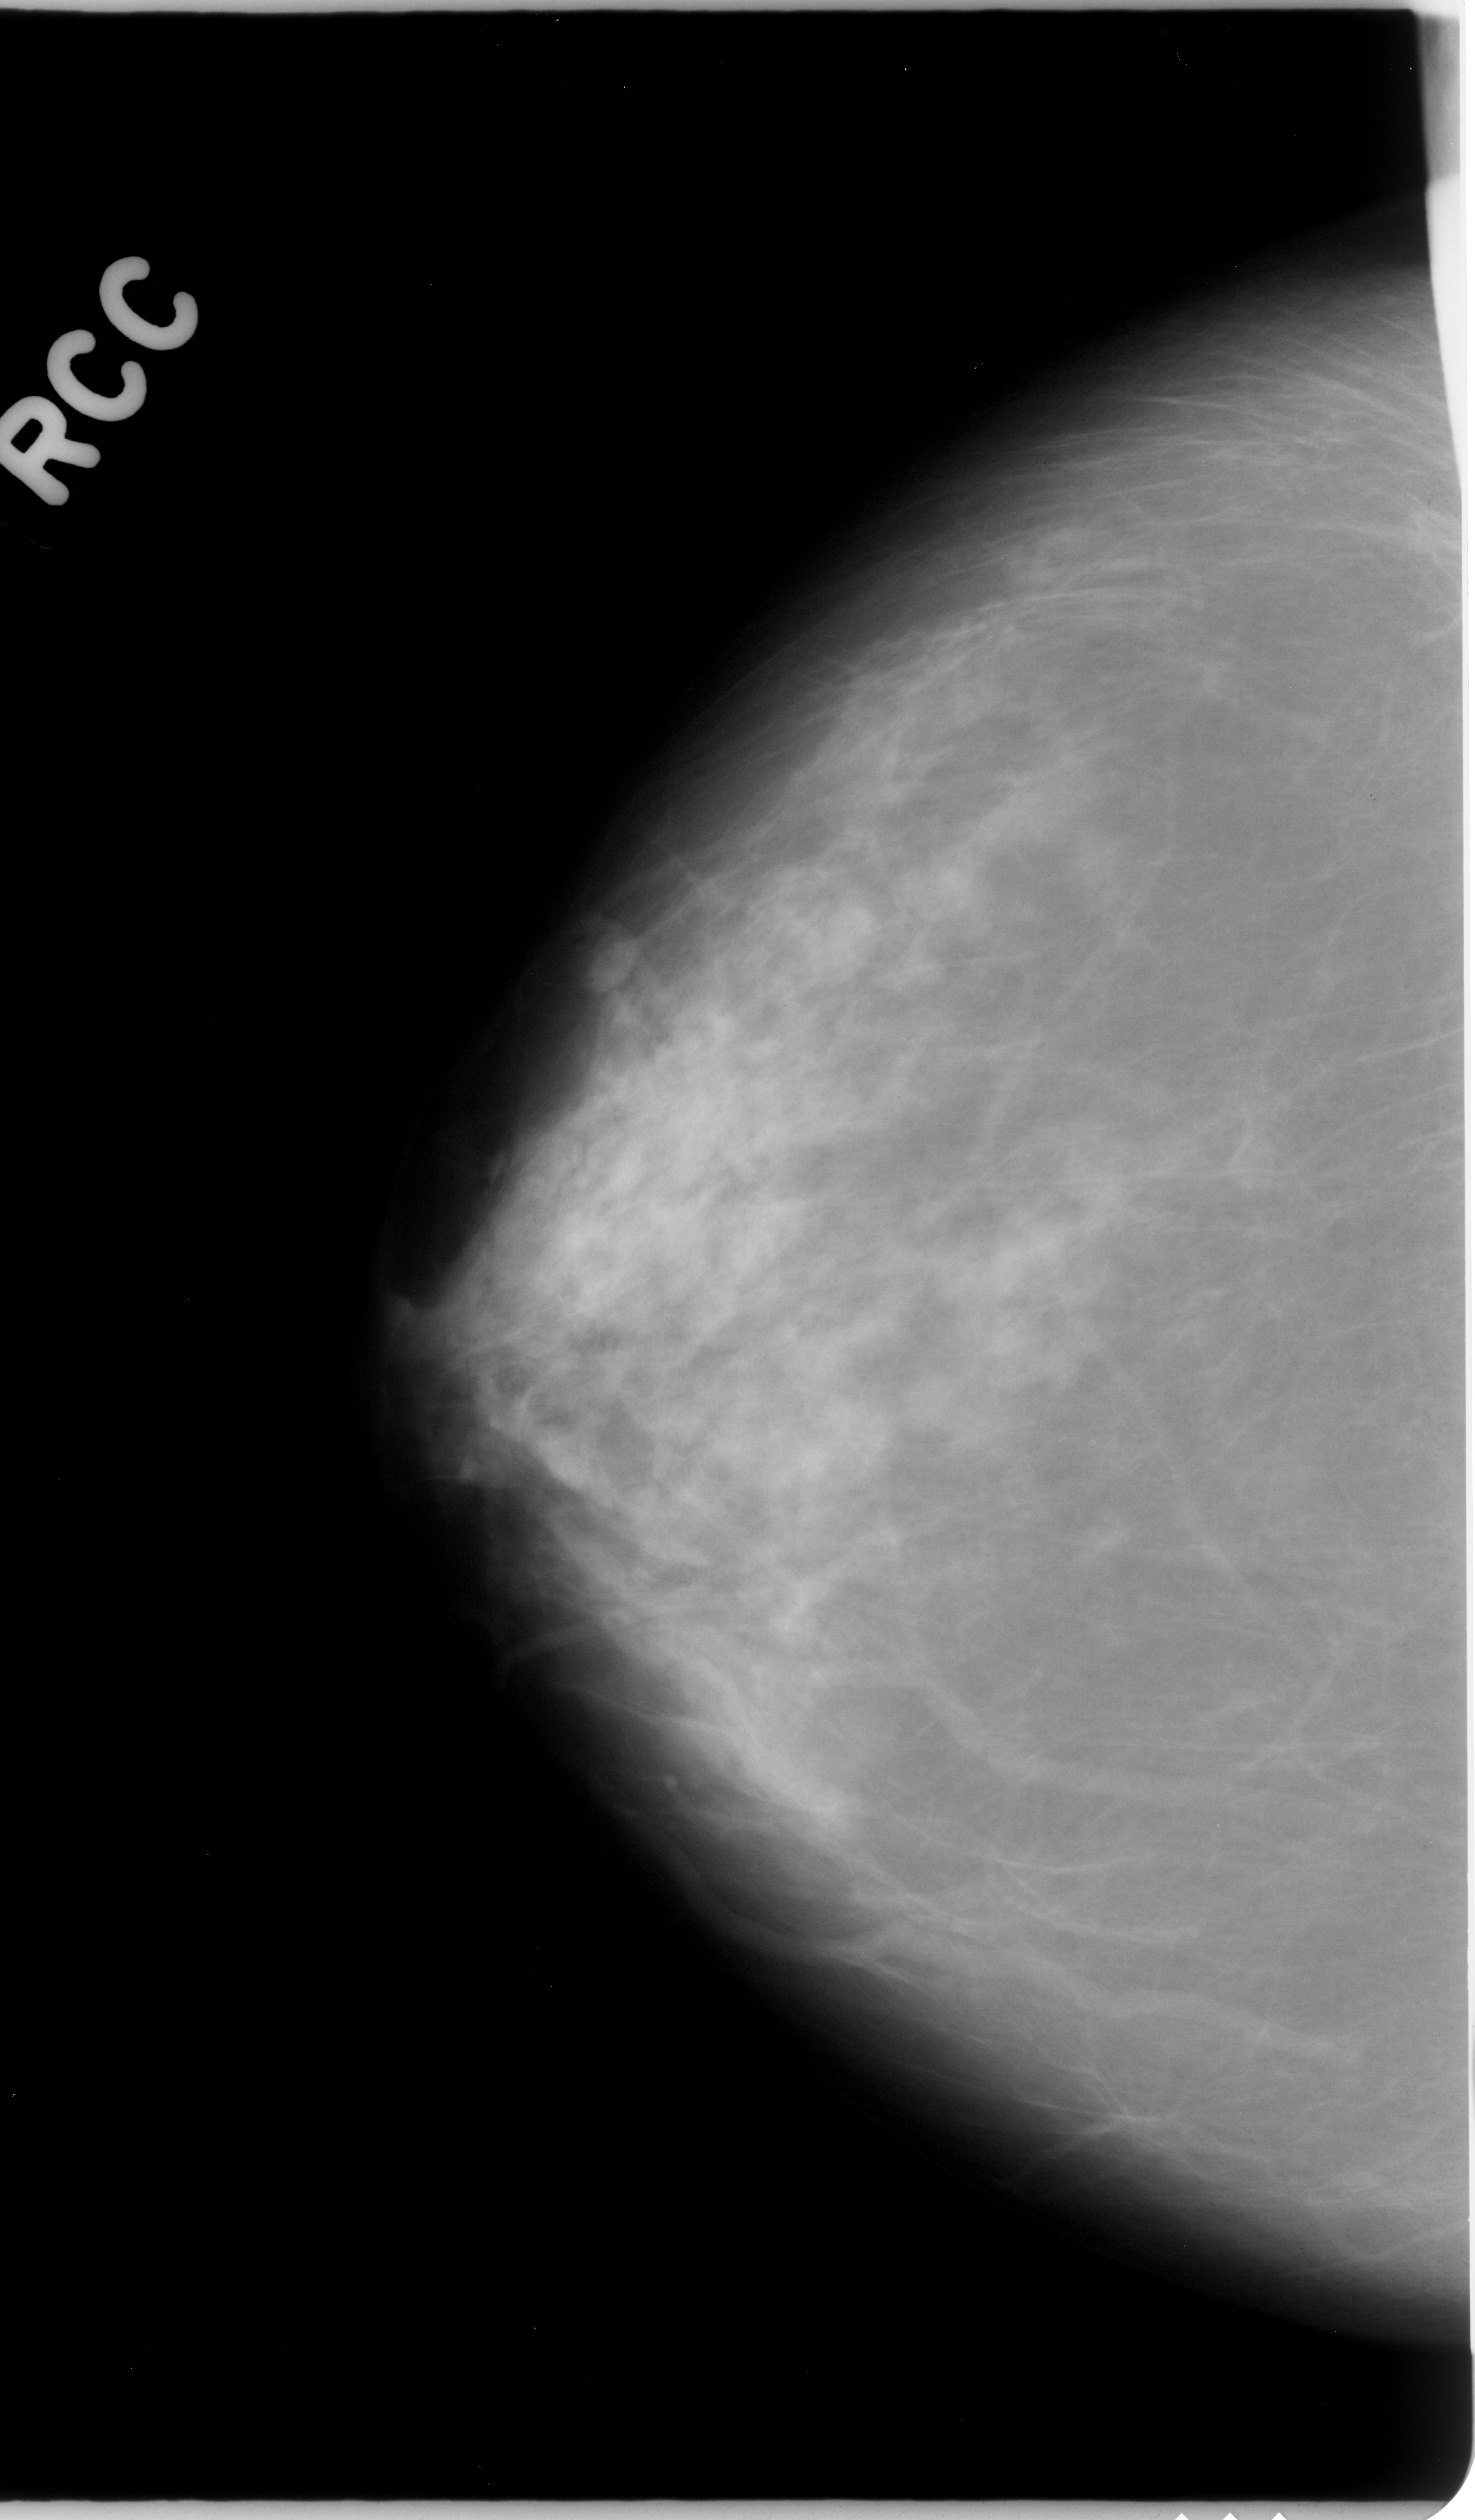
Scanned film-screen mammogram; right breast; craniocaudal (CC) view; BI-RADS breast density category 2 (scale 1–4).
Marked abnormality: mass, shape lobulated, margins circumscribed; BI-RADS assessment category 3; pathology (as recorded): benign.